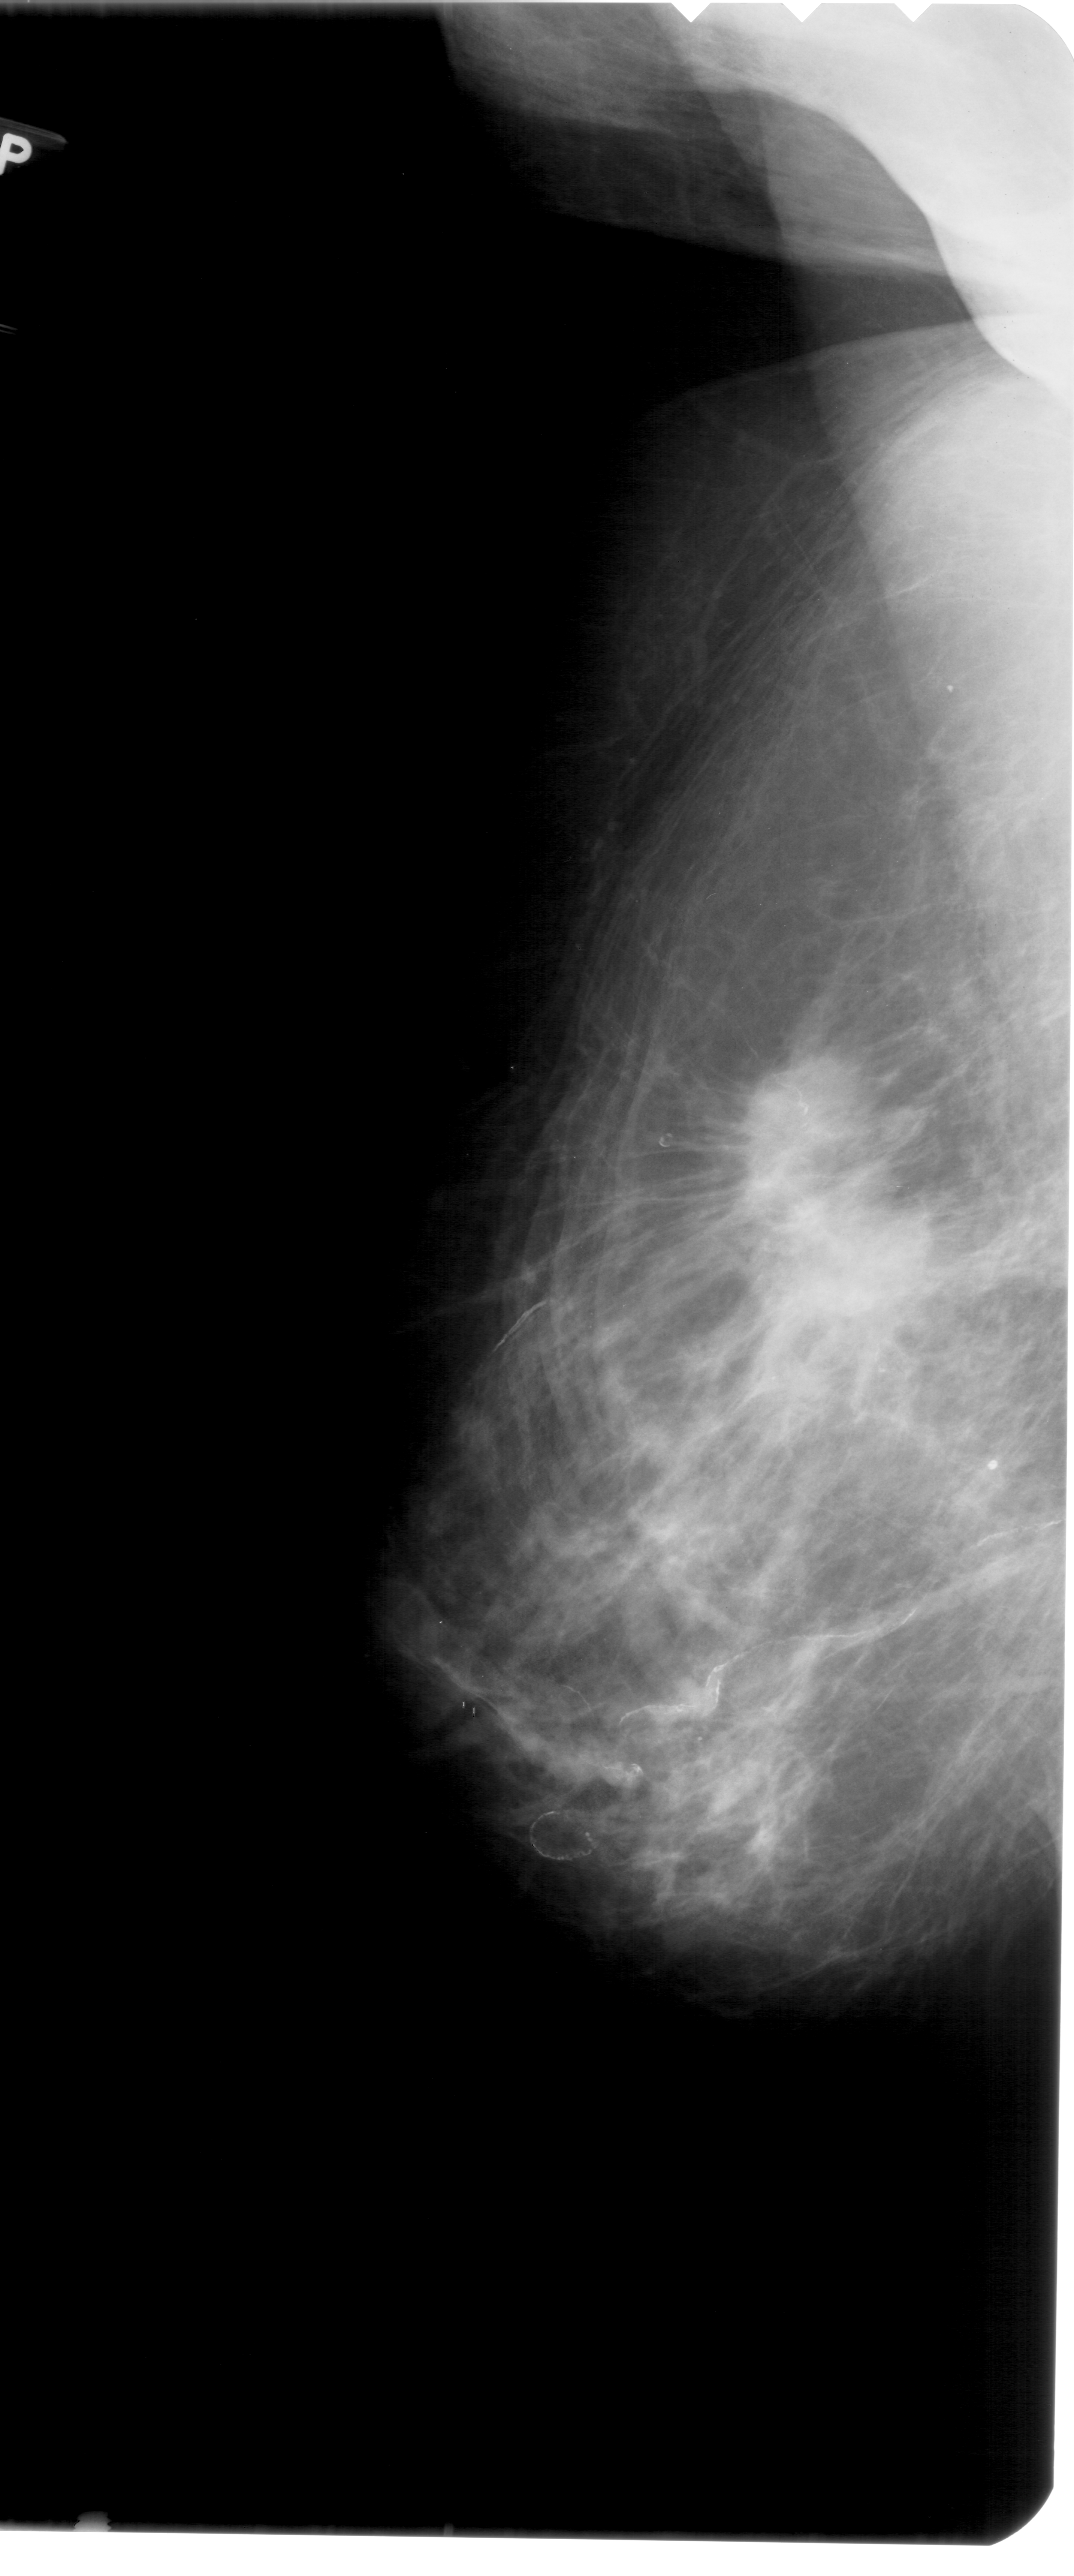
Digitized screen-film mammogram, left breast, mediolateral oblique (MLO) view, BI-RADS breast density category 3 (scale 1–4).
Mass, shape irregular, margins spiculated; BI-RADS assessment category 5; pathology (as recorded): malignant.